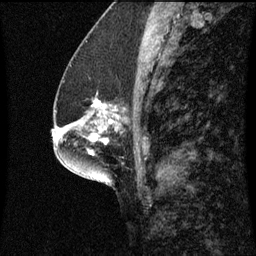
Breast MRI (dynamic contrast-enhanced), one sagittal slice. Slice 26 of 60 in the series (ordered by position). Dynamic contrast-enhanced series, image 2 of 3 at this slice position (ordered by acquisition). 1.5 T. TE 4.2 ms, TR 8.9 ms. 2 mm slice thickness. 256 × 256 image matrix, field of view 200 × 200 mm. Female patient, age 57 years. From the clinical record (not read from this slice): setting: breast cancer imaged before/during neoadjuvant chemotherapy; receptor status: HR-positive, HER2-negative.
Structures marked on this image (semi-automatically segmented with operator editing):
- analysis volume of interest (the breast-tissue region the enhancement analysis was run in; not a lesion): bounding box <82,94,124,125> (left, top, right, bottom; pixels)
- tumour enhancement mask (voxels above the 70 % enhancement threshold inside the analysis volume of interest): <94,100,115,123>